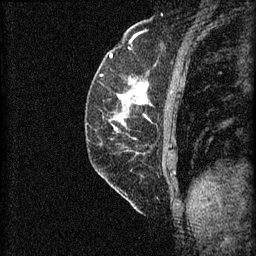
Breast MRI (dynamic contrast-enhanced), one sagittal slice; position 21 of 60 along the scan axis; 3 images stored at this slice position (order not interpretable as contrast timing); 1.5 T; TE 4.2 ms, TR 8.2 ms; 2 mm slice thickness; 256 × 256 image matrix, field of view 180 × 180 mm. Female patient, age 59 years.
Annotated regions visible in this slice (semi-automatically segmented with operator editing):
- analysis volume of interest (the breast-tissue region the enhancement analysis was run in; not a lesion): box from (x=94, y=74) to (x=153, y=131) px
- tumour enhancement mask (voxels above the 70 % enhancement threshold inside the analysis volume of interest): (x=119, y=82)–(x=149, y=117)